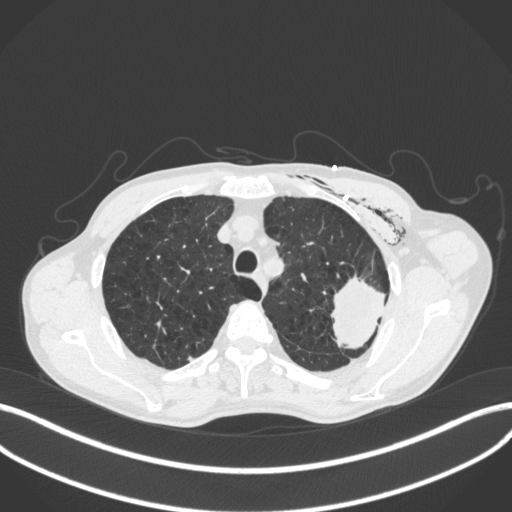
Chest CT, one axial slice. Position 323 of 416 along the scan axis. Reconstruction kernel B31f. 120 kVp. Lung window (W 1500 / L -600 HU). 1 mm slice thickness. 512 × 512 image matrix. Male patient, age 58 years. From the clinical record (not read from this slice): clinical TNM (as recorded): T3 N0 M0.
Annotated regions visible in this slice (bounding box drawn by a radiologist):
- lung tumour (recorded histology: adenocarcinoma): bounding box [x1, y1, x2, y2] px = [322, 270, 394, 352]